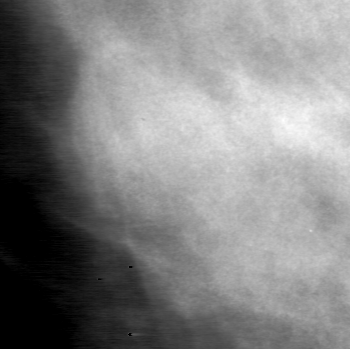
Region of interest cut from a scanned film mammogram (one marked finding); right breast; CC view.
Finding: mass, shape oval, margins obscured; BI-RADS assessment category 0; subtlety rating 4 on a 1 (subtle) to 5 (obvious) scale; pathology (as recorded): benign.